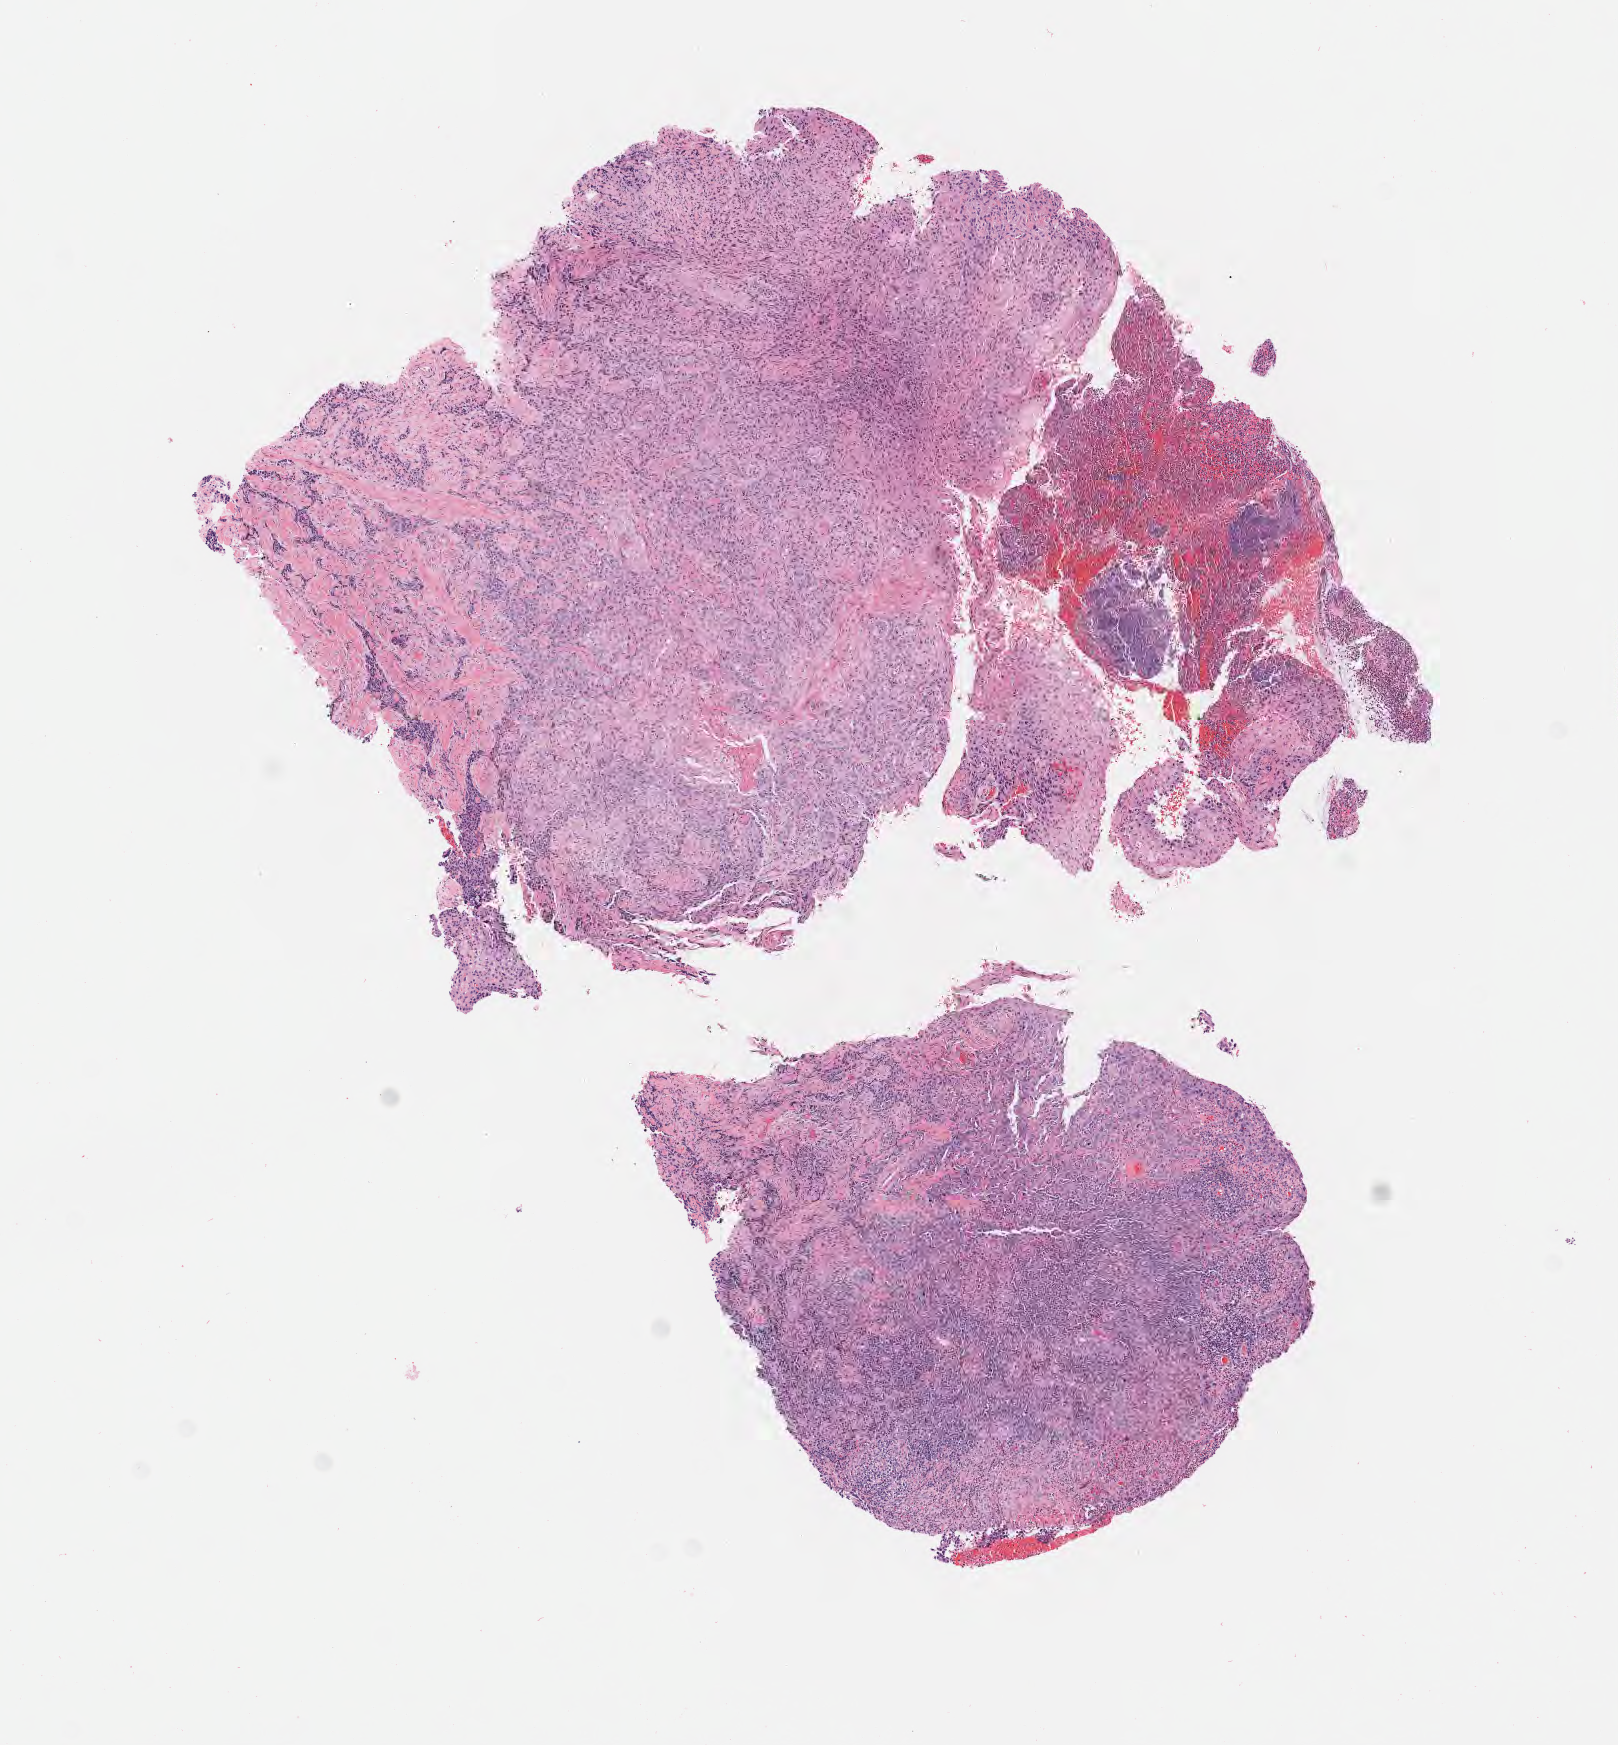
Digitized hematoxylin and eosin (H&E)-stained section, a low-resolution overview of the entire scanned area, about 6.5 x 7.1 mm; specimen: tumor tissue; site: cervix. Patient: female, aged 41.
Diagnosis: Squamous cell carcinoma, keratinizing, NOS.